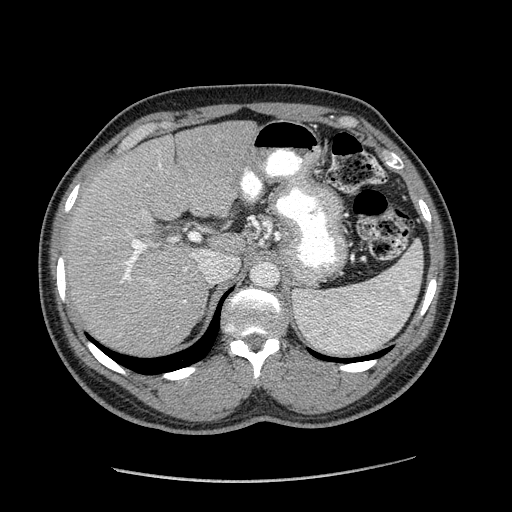
Contrast-enhanced abdominal CT (liver protocol), one axial slice. Slice 123 of 182 in the series (ordered by position). Soft-tissue window (W 400 / L 40 HU). 2.5 mm slice thickness. 512 × 512 image matrix, field of view 400 × 400 mm. From the clinical record (not read from this slice): diagnosis: hepatocellular carcinoma (patient treated with transarterial chemoembolisation; whether this scan precedes or follows treatment is not stated here); TNM stage (as recorded): Stage-I; Child-Pugh class: A; tumour differentiation: well differentiated.
Structures marked on this image (semi-automatically segmented with operator editing):
- liver parenchyma outside the tumour (the mass and vessels are separate outlines, so this box may not span the whole liver): box from (x=64, y=120) to (x=256, y=354) px
- liver vessels: (x=103, y=163)–(x=199, y=303)